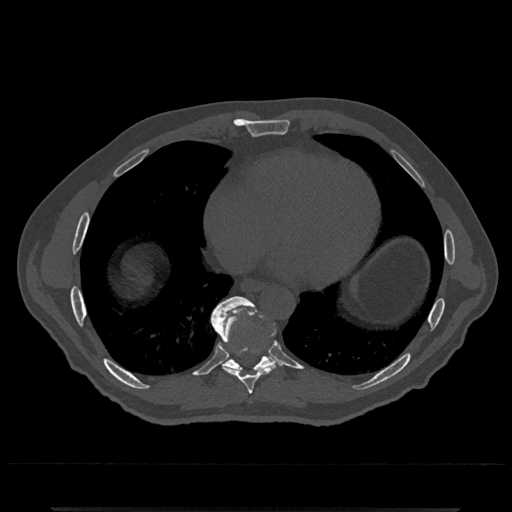
CT including the spine, one axial slice. Slice 645 of 797 in the series (ordered by position). 120 kVp. Bone window (W 1800 / L 400 HU). 0.5 mm slice thickness. 512 × 512 image matrix, field of view 393 × 393 mm. Patient: male, 67 years. Case-level facts recorded for this patient, not image findings: primary cancer: prostate.
Outlined on this slice (semi-automatic segmentation, software-assisted and operator-edited):
- T8 vertebra: box from (x=212, y=322) to (x=280, y=394) px
- T9 vertebra: (x=210, y=296)–(x=278, y=372)